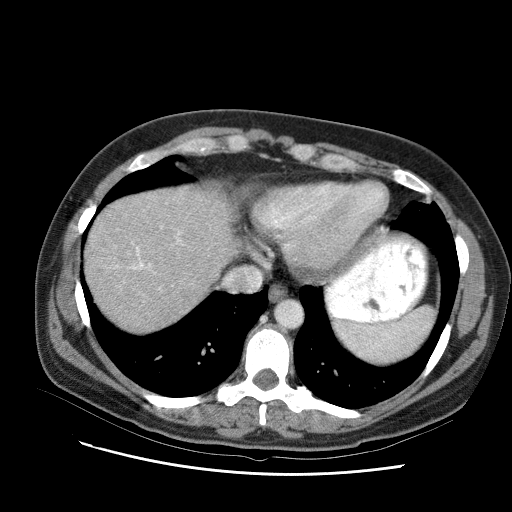
Contrast-enhanced abdominal CT (liver protocol), one axial slice; position 83 of 95 along the scan axis; reconstruction kernel STANDARD; one of 2 acquisitions stored at this slice position; soft-tissue window (W 400 / L 40 HU); 2.5 mm slice thickness; 512 × 512 image matrix. From the clinical record (not read from this slice): diagnosis: hepatocellular carcinoma (patient treated with transarterial chemoembolisation; whether this scan precedes or follows treatment is not stated here); TNM stage (as recorded): Stage-I; Child-Pugh class: B.
Structures marked on this image (semi-automatically segmented with operator editing):
- liver parenchyma outside the tumour (the mass and vessels are separate outlines, so this box may not span the whole liver): bounding box [x1, y1, x2, y2] px = [90, 194, 214, 308]
- liver vessels: [135, 236, 138, 239]